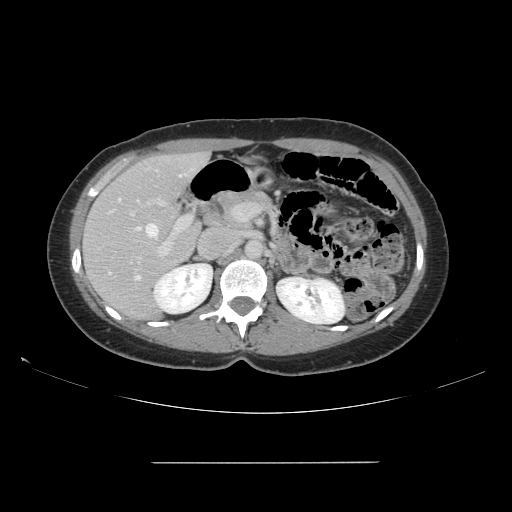
Contrast-enhanced abdominal CT, one axial slice. Slice 88 of 151 in the series (ordered by position). 120 kVp. Soft-tissue window (W 400 / L 40 HU). 512 × 512 image matrix. Female patient, age 46 years. From the clinical record (not read from this slice): diagnosis: colorectal cancer liver metastases, imaged before liver resection; multiple liver metastases: yes; largest metastasis: 3 cm; disease in both lobes: yes.
Structures marked on this image (manually delineated by an expert):
- hepatic veins: box from (x=118, y=175) to (x=182, y=279) px
- liver: (x=84, y=154)–(x=208, y=321)
- planned liver remnant (the part of the liver to remain after resection): (x=93, y=154)–(x=202, y=294)
- portal vein (with intrahepatic branches): (x=129, y=197)–(x=246, y=258)